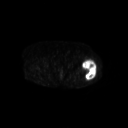
FDG PET of an extremity soft-tissue mass (from a PET/CT study), one axial slice; slice 245 of 267 in the series (ordered by position); 128 × 128 image matrix. Patient: female, 62 years. Case-level facts recorded for this patient, not image findings: histological type: undifferentiated – high grade; grade: high; site of the primary tumour: left thigh.
Outlined on this slice (expert contour drawn on MRI and transferred to this co-registered scan by the dataset authors):
- gross tumour volume including surrounding oedema: bounding box (x1, y1, x2, y2) in pixels: (81, 59, 97, 81)
- gross tumour volume (mass): (81, 61, 96, 81)